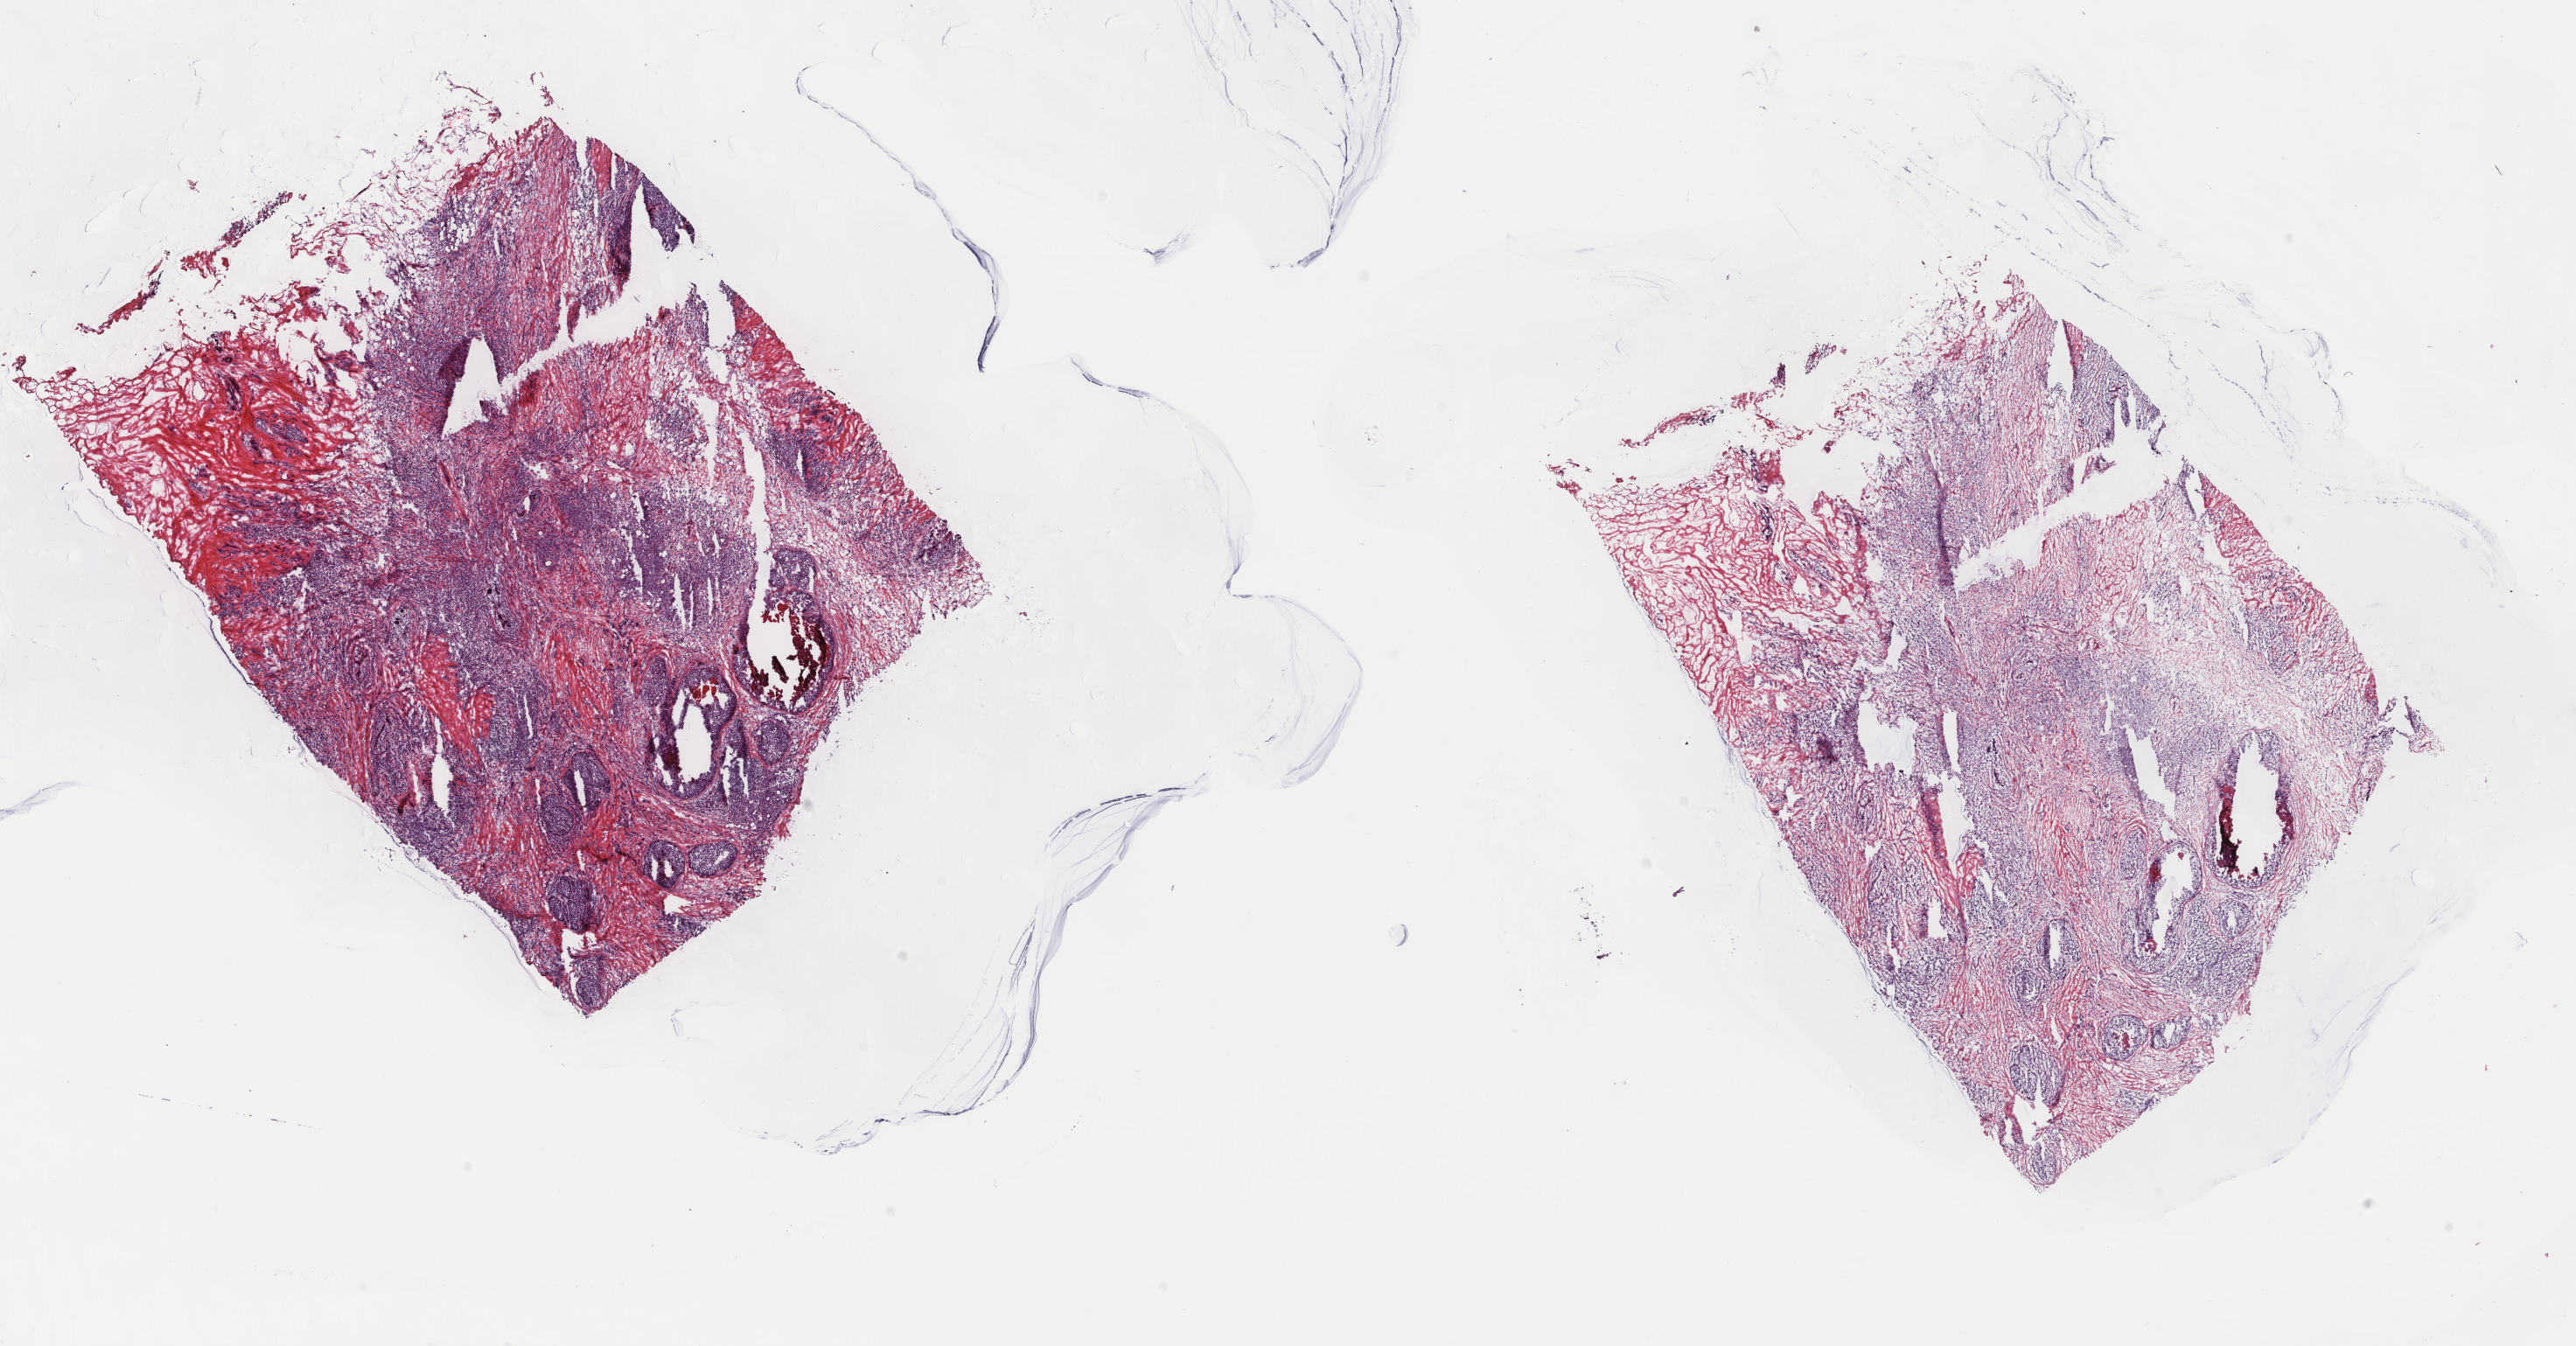
Whole-slide histology image, H&E — a low-resolution overview of the entire scanned area, about 23.4 x 12.2 mm, frozen section from the top of the tissue portion, breast, primary tumour sample. Patient: female, age at initial diagnosis 49 years. Slide review estimates, as recorded: tumour cells 60%, tumour nuclei 60%, normal cells 0%, stromal cells 30%, necrosis 10%. Infiltration values recorded for this section: lymphocyte infiltration 40%, monocyte infiltration 10%, neutrophil infiltration 10%.
* TNM: T2 N3a M0
* lymph nodes positive (case pathology): 27 of 27 examined
* histologic diagnosis: Lobular carcinoma, NOS
* AJCC pathologic stage: IIIC (7th edition)